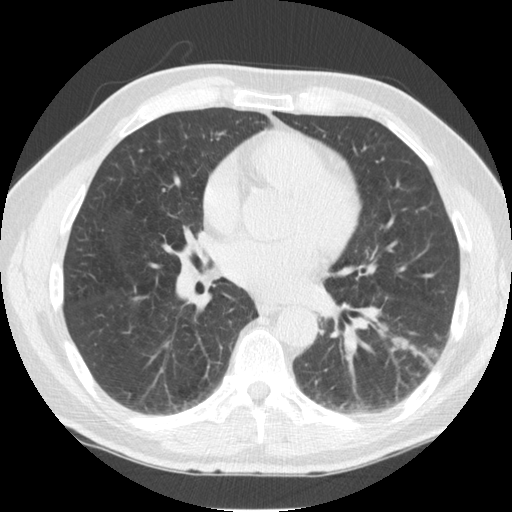
Axial slice from a low-dose chest CT screening exam; third annual screen; lung window (W 1500 / L -600 HU); standard (soft-tissue) reconstruction kernel (STANDARD); slice 74 of 126 in the series; 512 × 512 image matrix, field of view 344 × 344 mm. Male, age 57 years at enrolment.
Lesion marked by an expert reader, bounding box (x1, y1, x2, y2) in pixels: (410, 327, 455, 372). Screening reader's record for this exam (one nodule recorded; not confirmed to be the boxed lesion): non-calcified nodule or mass ≥4 mm, left lower lobe, 13 × 12 mm, spiculated (stellate) margins, soft tissue attenuation, pre-existing on the prior screen: yes; interval growth: yes. Official screen result: positive, other.